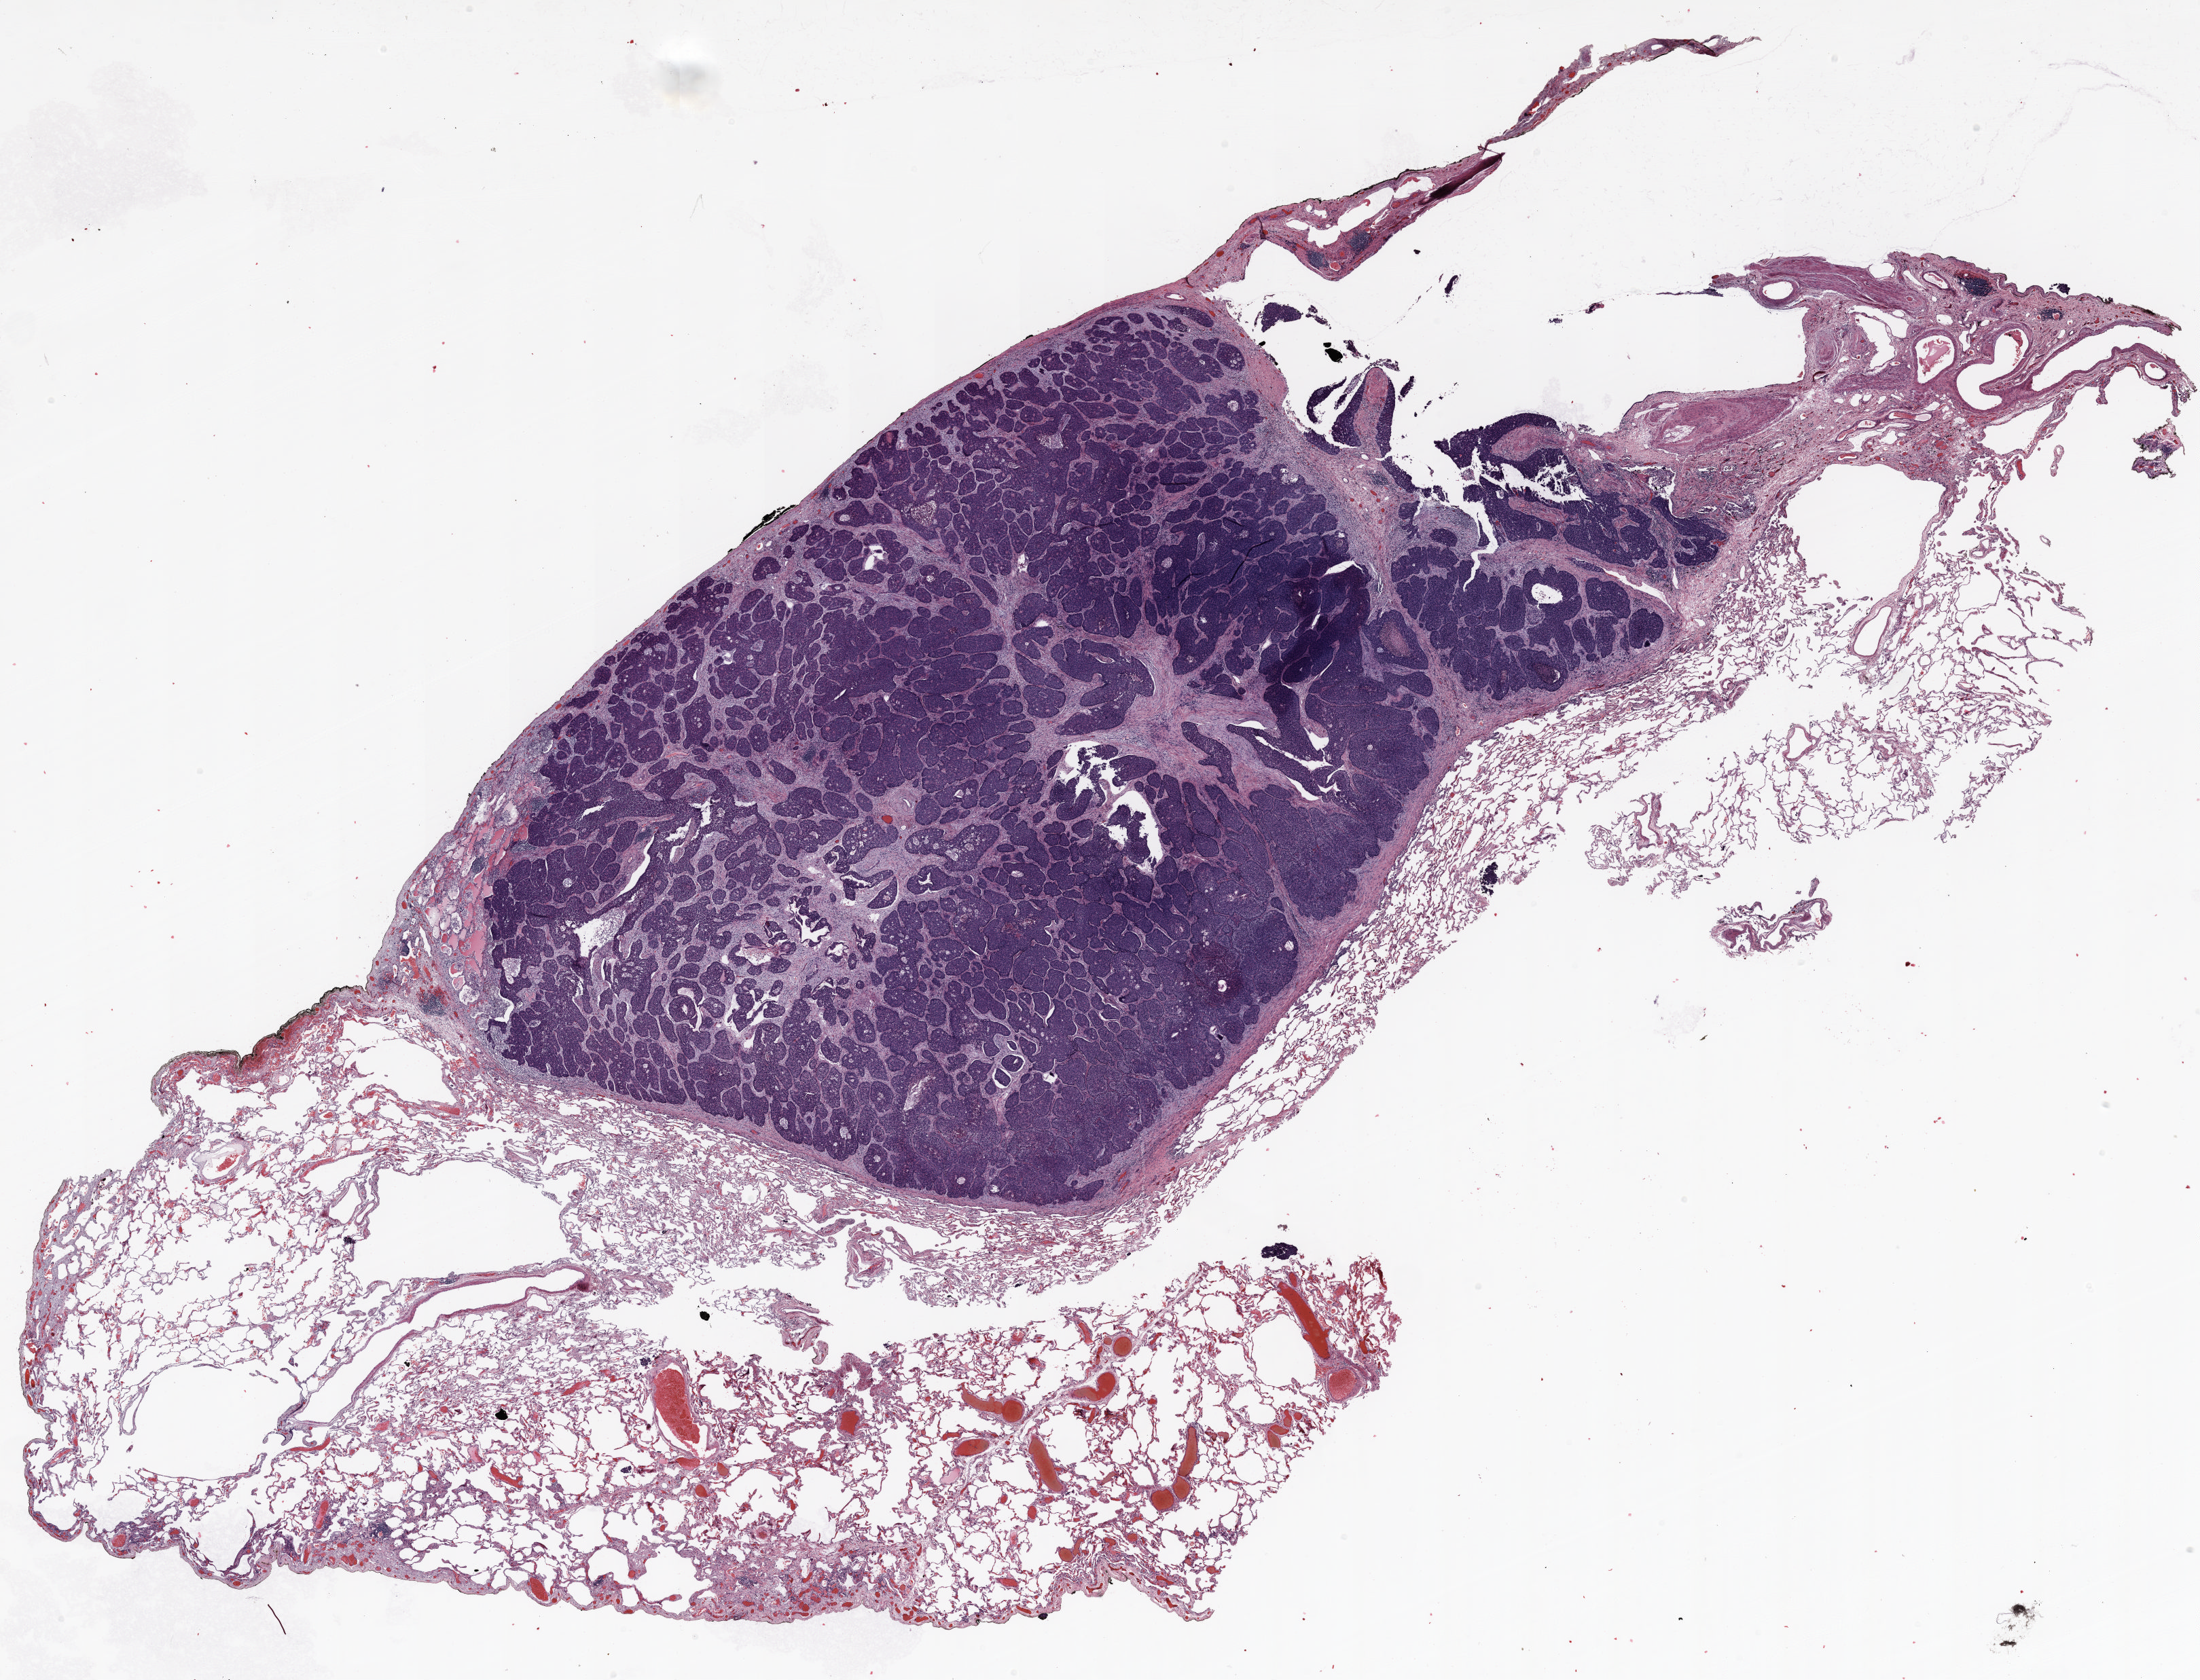
Whole-slide histology image, H&E, whole scanned area (about 26.0 x 19.9 mm) shown as a low-resolution overview, formalin-fixed paraffin-embedded (FFPE) section, lung tissue. Female patient, aged 74 at enrolment. Former smoker at enrolment. Grade: poorly differentiated (G3).
* primary tumour location (clinical record): left upper lobe
* stage (AJCC 6th edition): IA
* tumour size (pathology): 24 mm
* participant's lung-cancer diagnosis: Adenocarcinoma, NOS (ICD-O-3 8140/3)